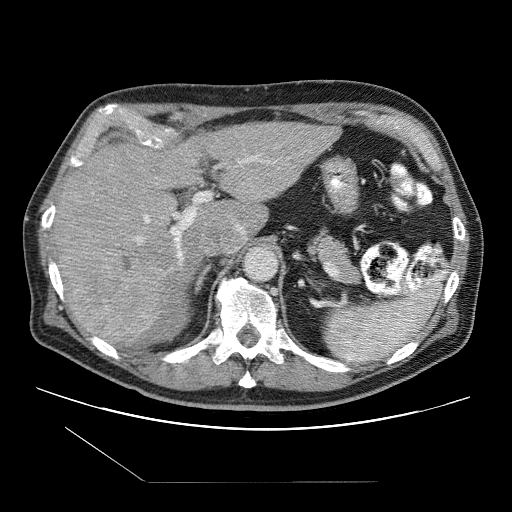
Contrast-enhanced abdominal CT (liver protocol), one axial slice. One of 2 acquisitions stored at this slice position. Soft-tissue window (W 400 / L 40 HU). 512 × 512 image matrix, field of view 400 × 400 mm. Case-level facts recorded for this patient, not image findings: diagnosis: hepatocellular carcinoma (patient treated with transarterial chemoembolisation; whether this scan precedes or follows treatment is not stated here); TNM stage (as recorded): Stage-IIIB; Child-Pugh class: A; tumour differentiation: well differentiated; tumour nodularity: multinodular.
Structures marked on this image (semi-automatic segmentation, software-assisted and operator-edited):
- abdominal aorta: bounding box (x1, y1, x2, y2) in pixels: (246, 248, 278, 280)
- liver parenchyma outside the tumour (the mass and vessels are separate outlines, so this box may not span the whole liver): (52, 122, 339, 344)
- mass: (57, 243, 166, 345)
- liver vessels: (135, 157, 269, 264)